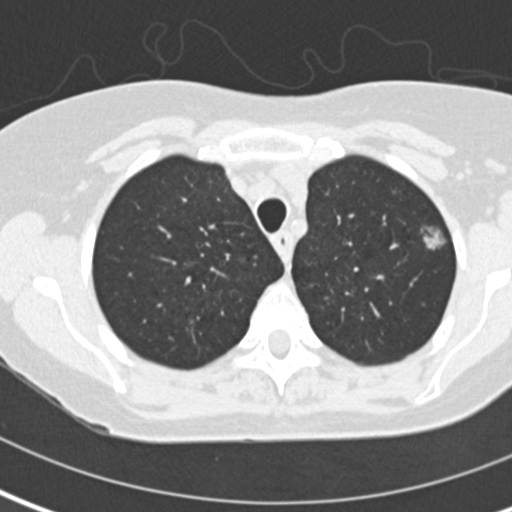
Chest CT (low-dose screening protocol), one axial image, second screening round (one year after baseline), lung window (W 1500 / L -600 HU), standard (soft-tissue) reconstruction kernel (B30f), 120 kVp, 512 × 512 image matrix. Female, age 60 years at enrolment. Former smoker at enrolment.
• Lesion marked by an expert reader, box from (x=414, y=224) to (x=465, y=264) px.
• The screening reader recorded 2 non-calcified nodules or masses ≥4 mm on this exam; which of them this box marks is not recorded.